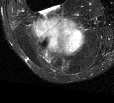
MRI of an extremity soft-tissue mass, one axial slice. Position 33 of 44 along the scan axis. T2-weighted fat-saturated. MR volume resampled by the dataset authors to the PET/CT grid (not the native acquisition matrix). 3.27 mm slice thickness. 114 × 103 image matrix. Female patient. Case-level facts recorded for this patient, not image findings: histological type: liposarcoma; site of the primary tumour: right thigh.
Outlined on this slice (expert contour drawn on MRI and transferred to this co-registered scan by the dataset authors):
- gross tumour volume (mass): box from (x=31, y=16) to (x=85, y=56) px